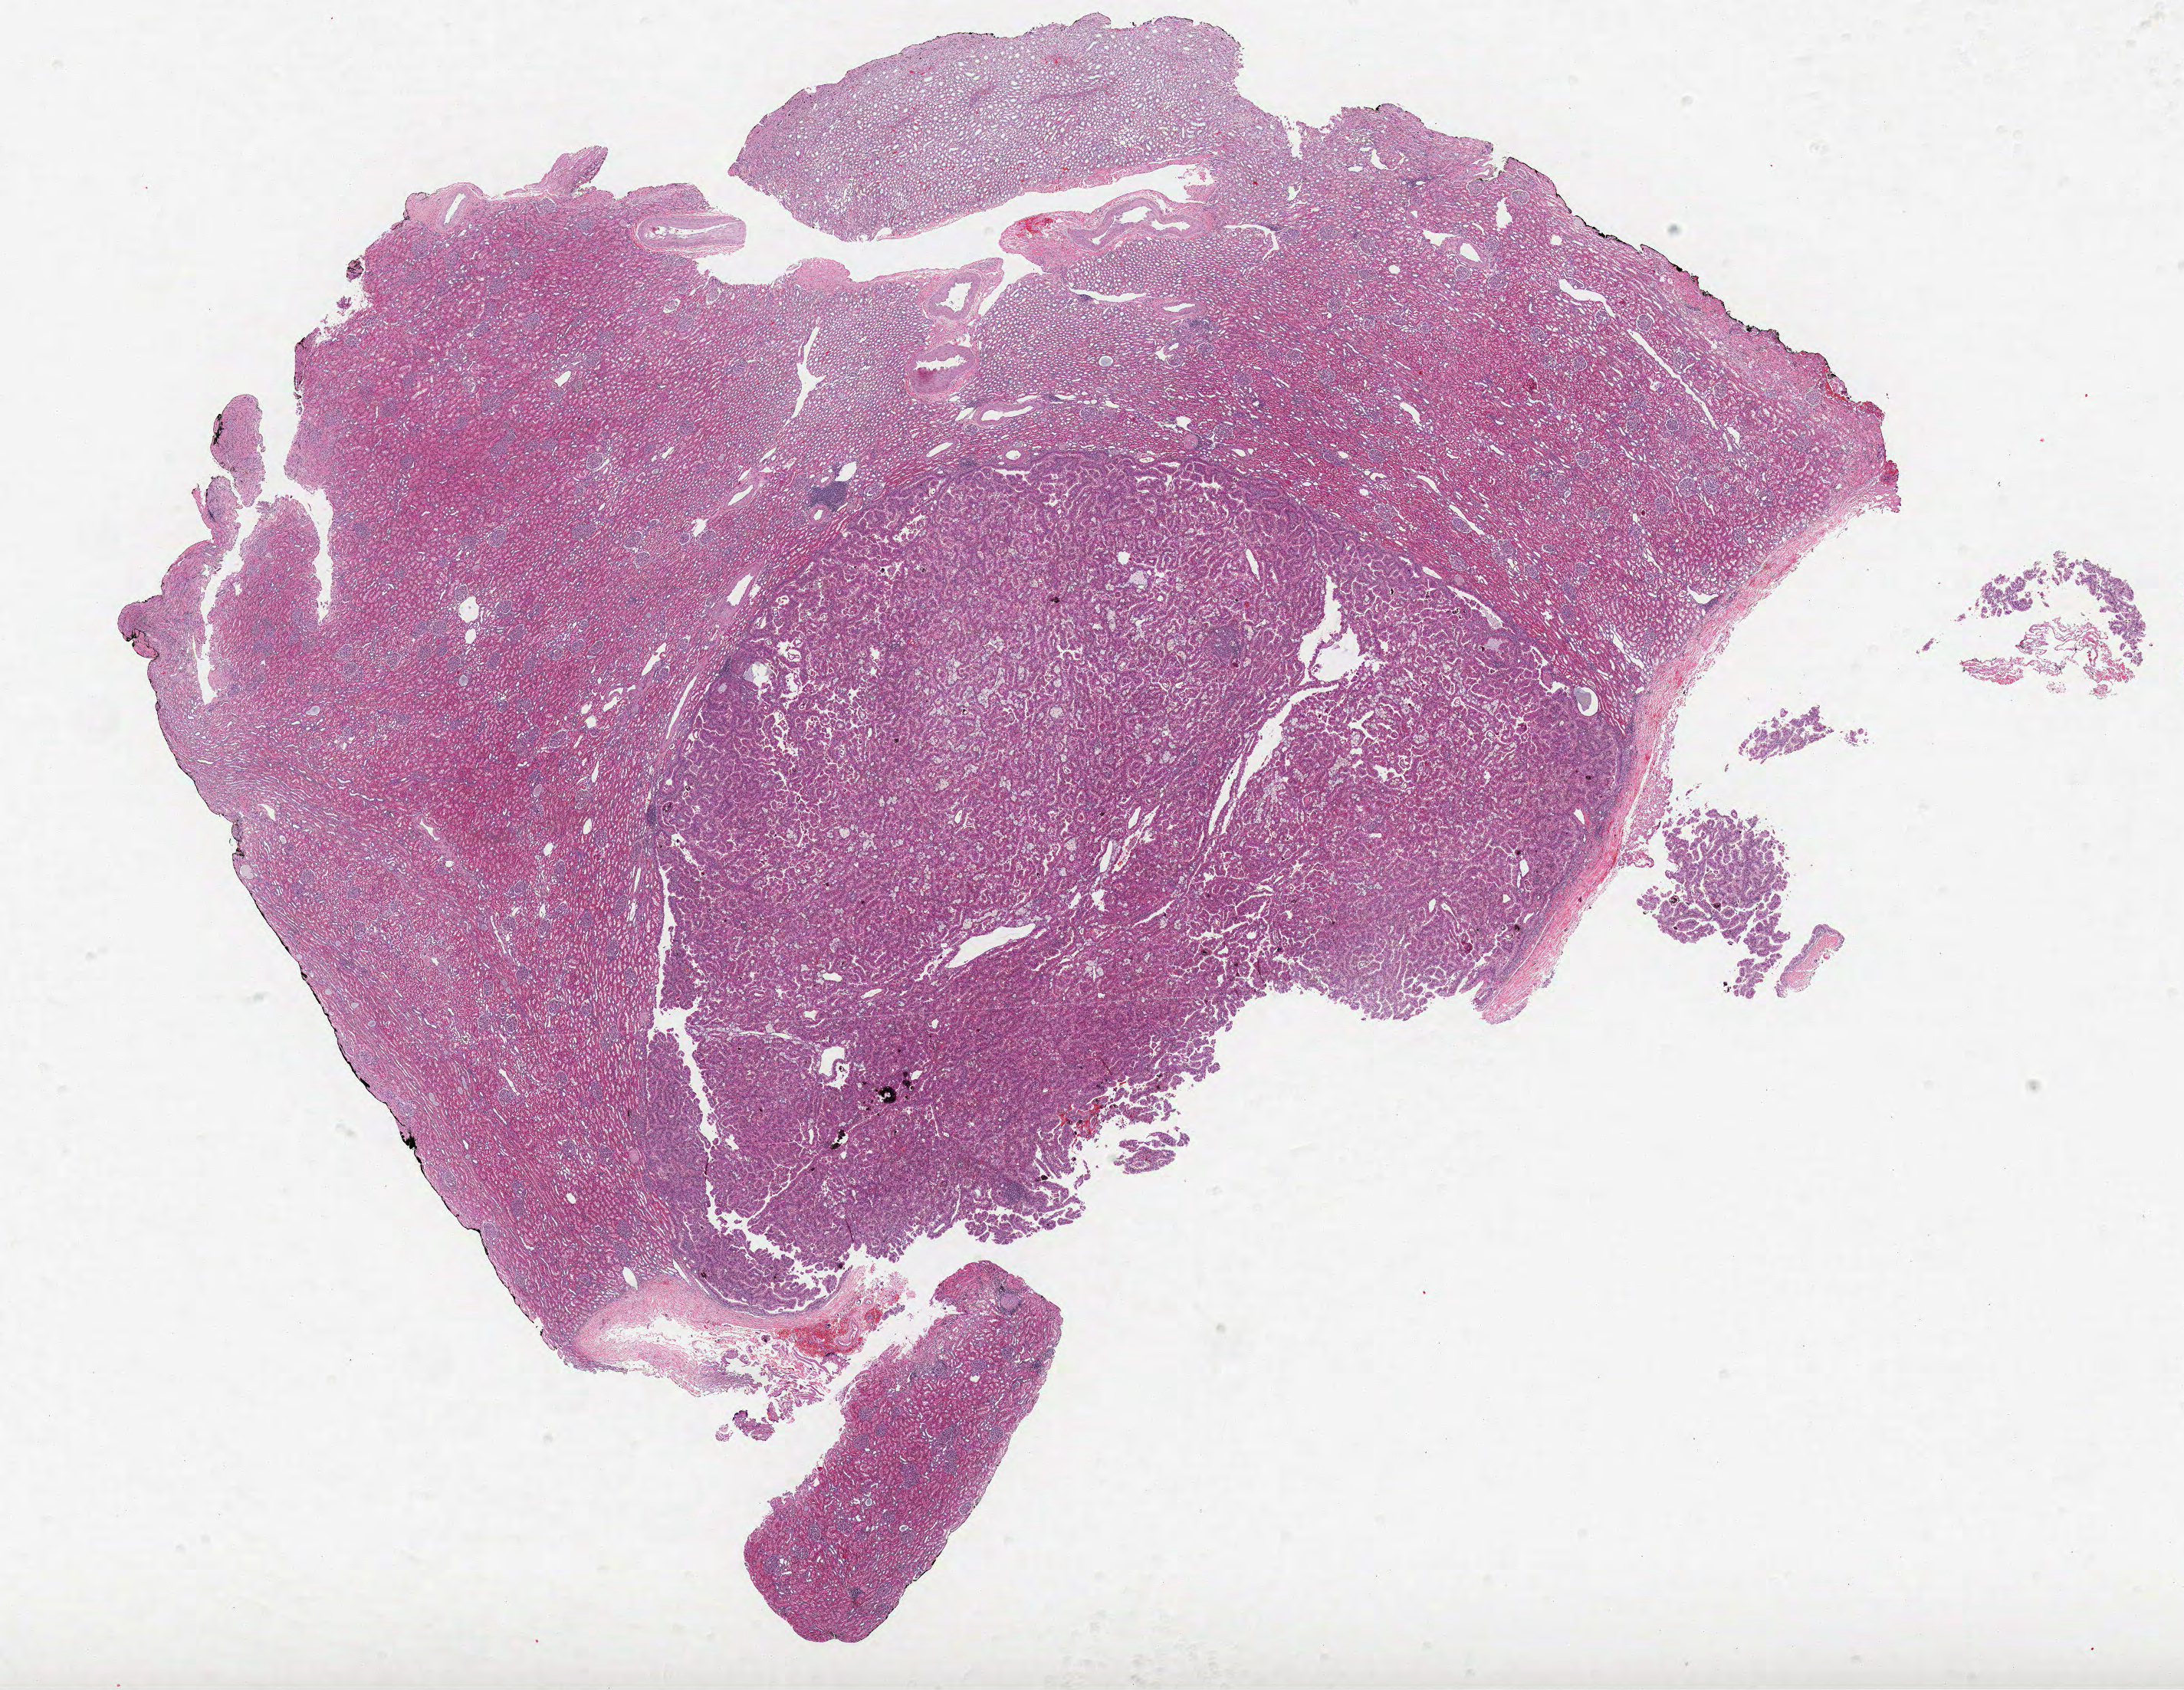
Whole-slide histology image, H&E-stained, shown as a low-resolution overview of the whole scanned area (about 22.8 x 17.6 mm, slide scanned at 40x). Formalin-fixed paraffin-embedded (FFPE) diagnostic section. Primary tumour sample from the kidney. Female patient; age at initial diagnosis 59 years.
Histologic diagnosis: Papillary adenocarcinoma, NOS.